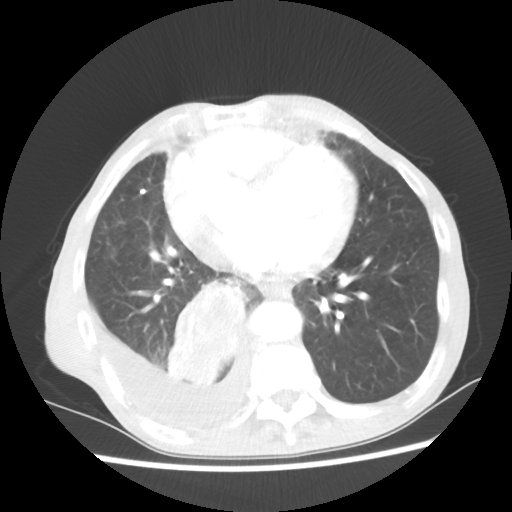
Chest CT, one axial slice. Reconstruction kernel STANDARD. 80 kVp. Lung window (W 1500 / L -600 HU). 5 mm slice thickness. 512 × 512 image matrix, field of view 335 × 335 mm. Patient: male, 76 years. From the clinical record (not read from this slice): clinical TNM (as recorded): T3 N3 M1a; histopathological grade: G3.
Structures marked on this image (bounding box drawn by a radiologist):
- lung tumour (recorded histology: squamous cell carcinoma): bounding box <162,278,252,389> (left, top, right, bottom; pixels)